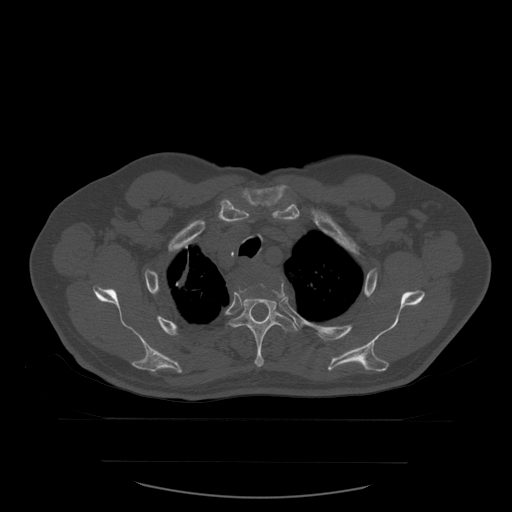
CT including the spine, one axial slice; bone window (W 1800 / L 400 HU); 1.25 mm slice thickness; 512 × 512 image matrix. Patient age 71 years. From the clinical record (not read from this slice): primary cancer: lung.
Annotated regions visible in this slice (semi-automatically segmented with operator editing):
- T3 vertebra: bounding box [x1, y1, x2, y2] px = [238, 279, 285, 295]
- T4 vertebra: [229, 283, 298, 368]